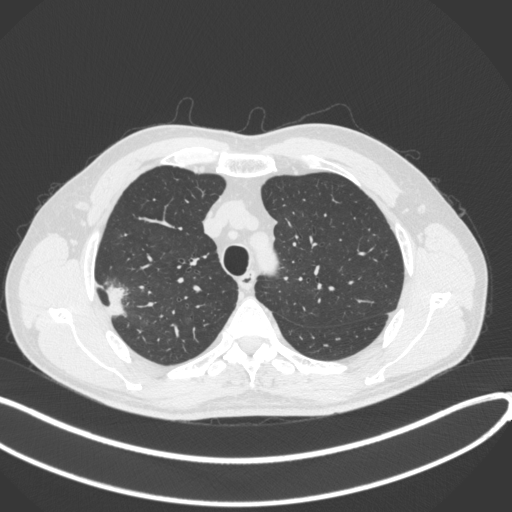
Chest CT, one axial slice; slice 327 of 381 in the series (ordered by position); reconstruction kernel B31f; lung window (W 1500 / L -600 HU); 1 mm slice thickness; 512 × 512 image matrix. Male patient, age 62 years. From the clinical record (not read from this slice): clinical TNM (as recorded): T1c N0 M0; histopathological grade: G2-3.
Outlined on this slice (rectangle marked by the reading radiologist):
- lung tumour (recorded histology: adenocarcinoma): bounding box [x1, y1, x2, y2] px = [101, 278, 130, 323]